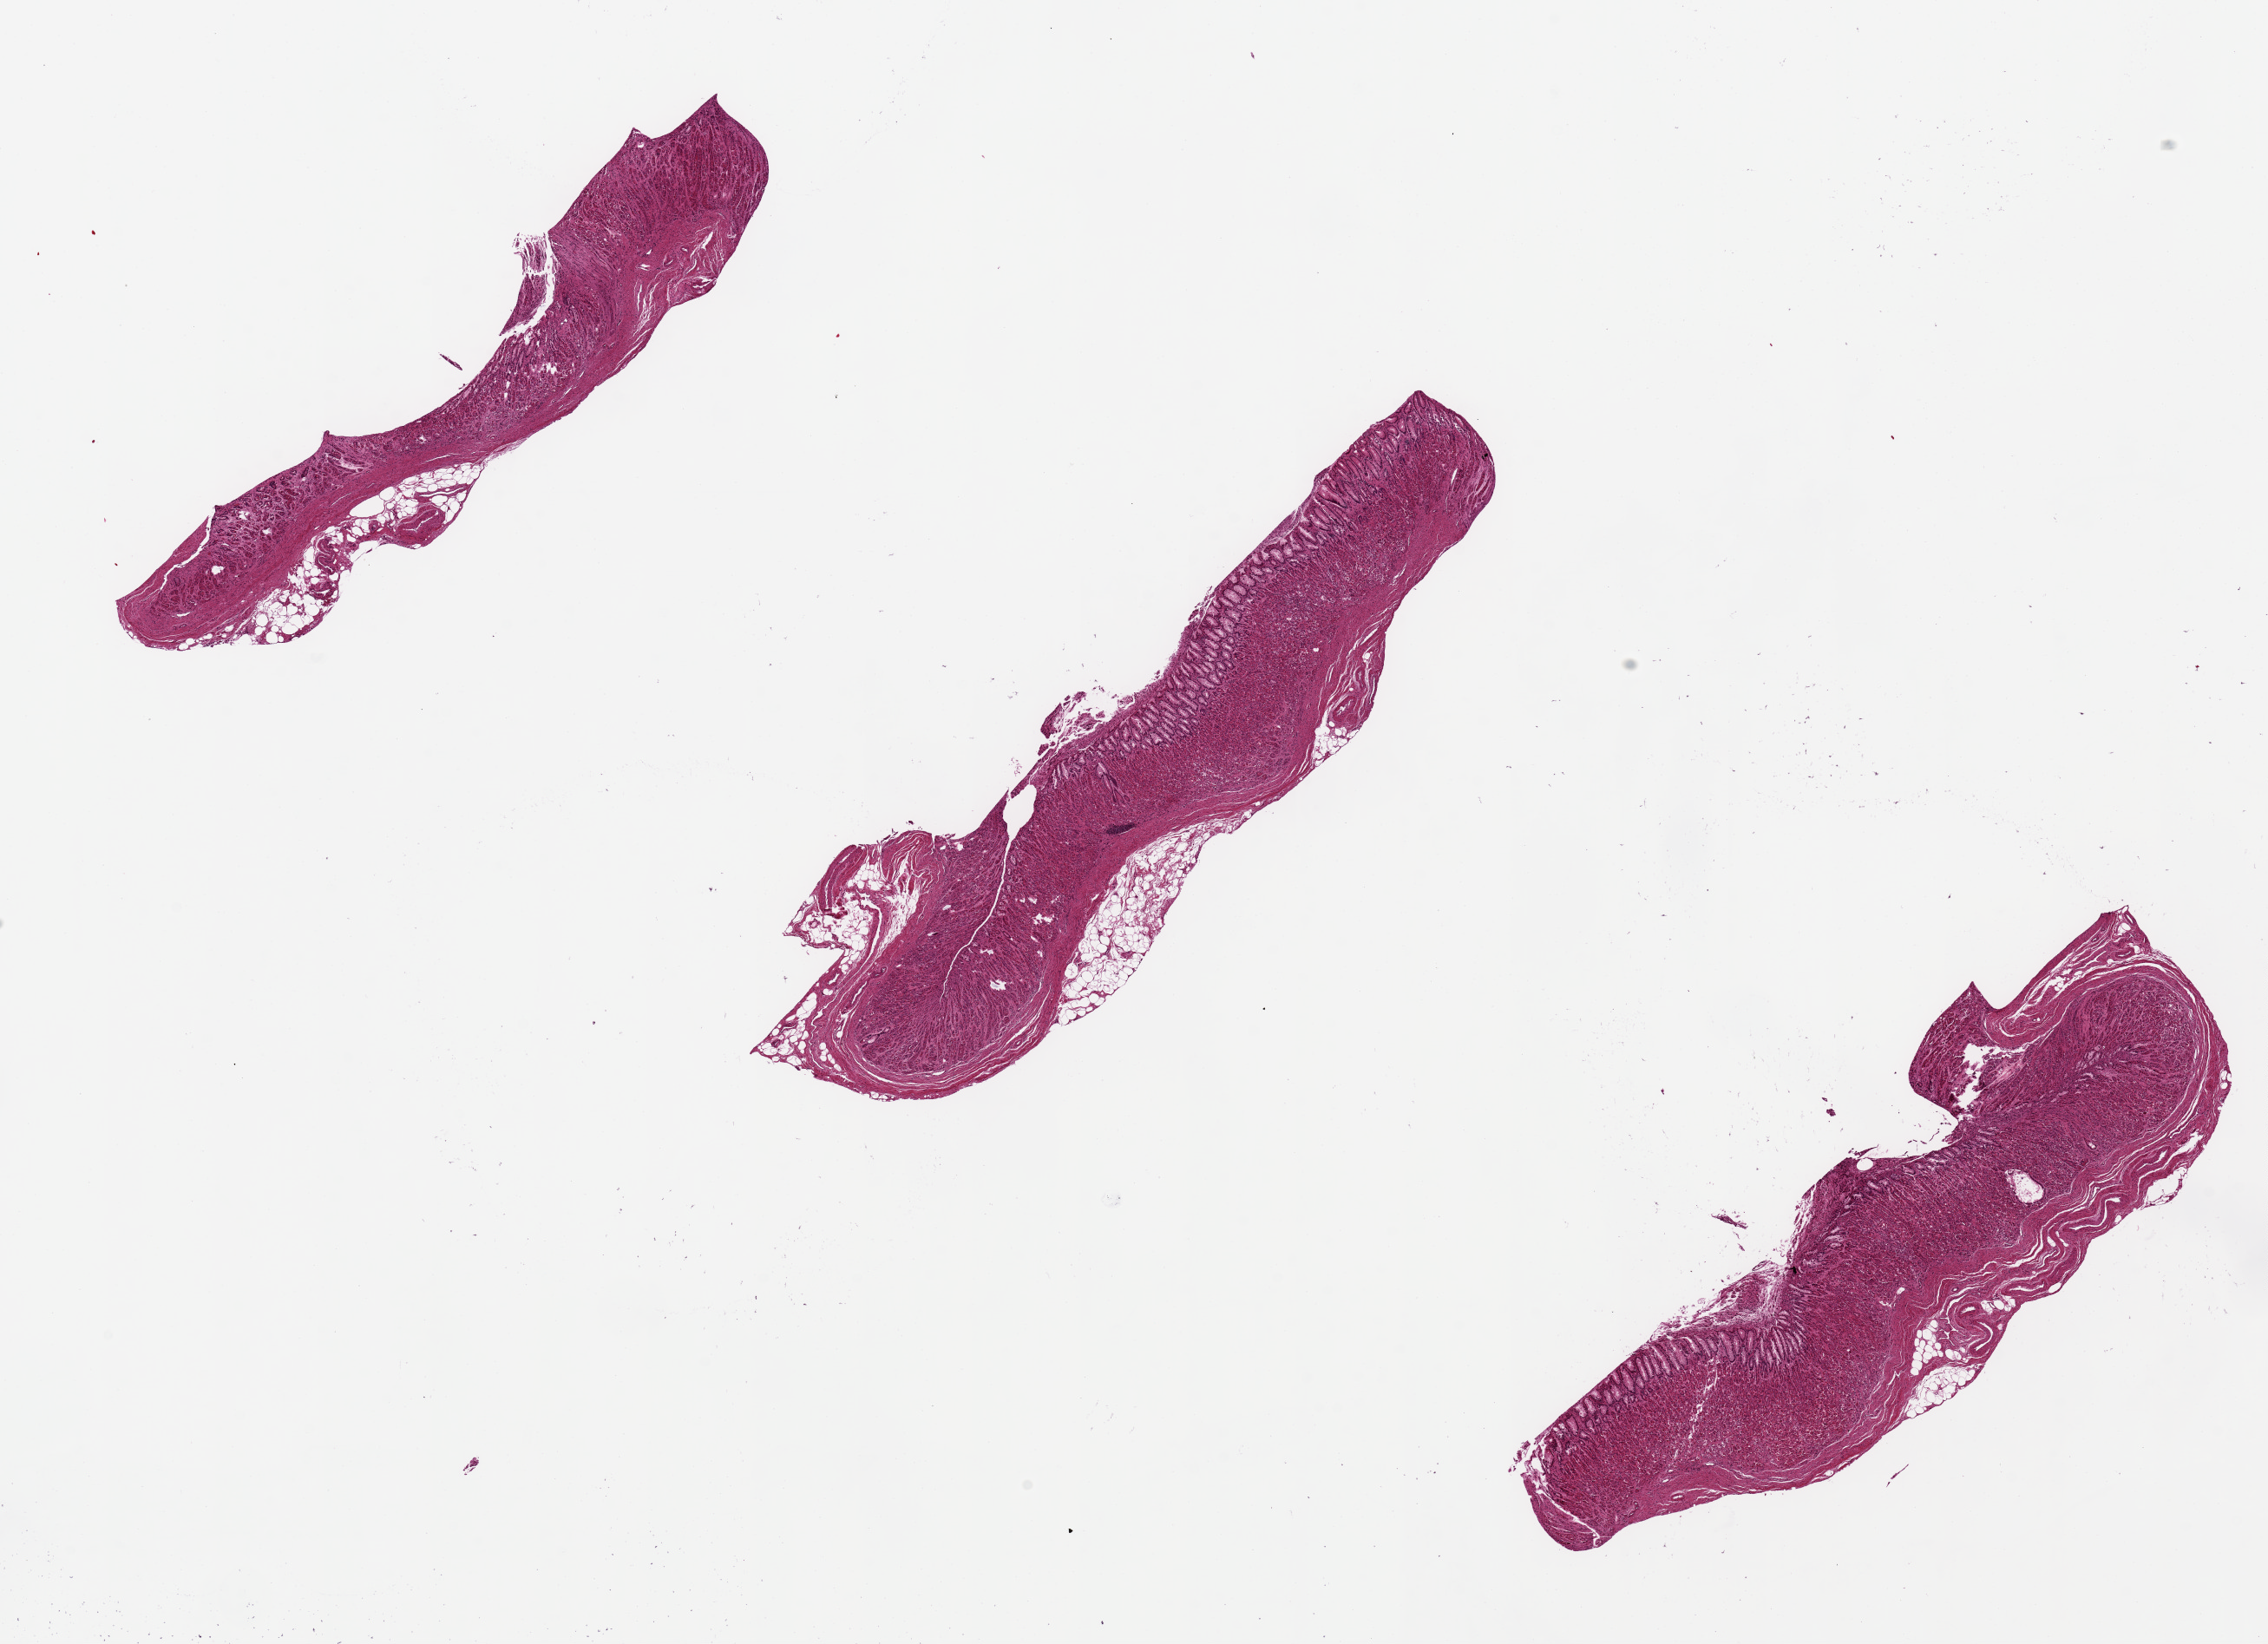
H&E whole-slide image, brightfield, shown as a low-resolution overview of the whole scanned area (about 20.7 x 15.0 mm, acquisition: 20x scan). PAXgene-fixed paraffin-embedded (PFPE) section. Section of stomach (target tissue). Donor tissue sample. Male donor.
Pathologist's review note for this sample: Mostly mucosa, no muscularis propria.